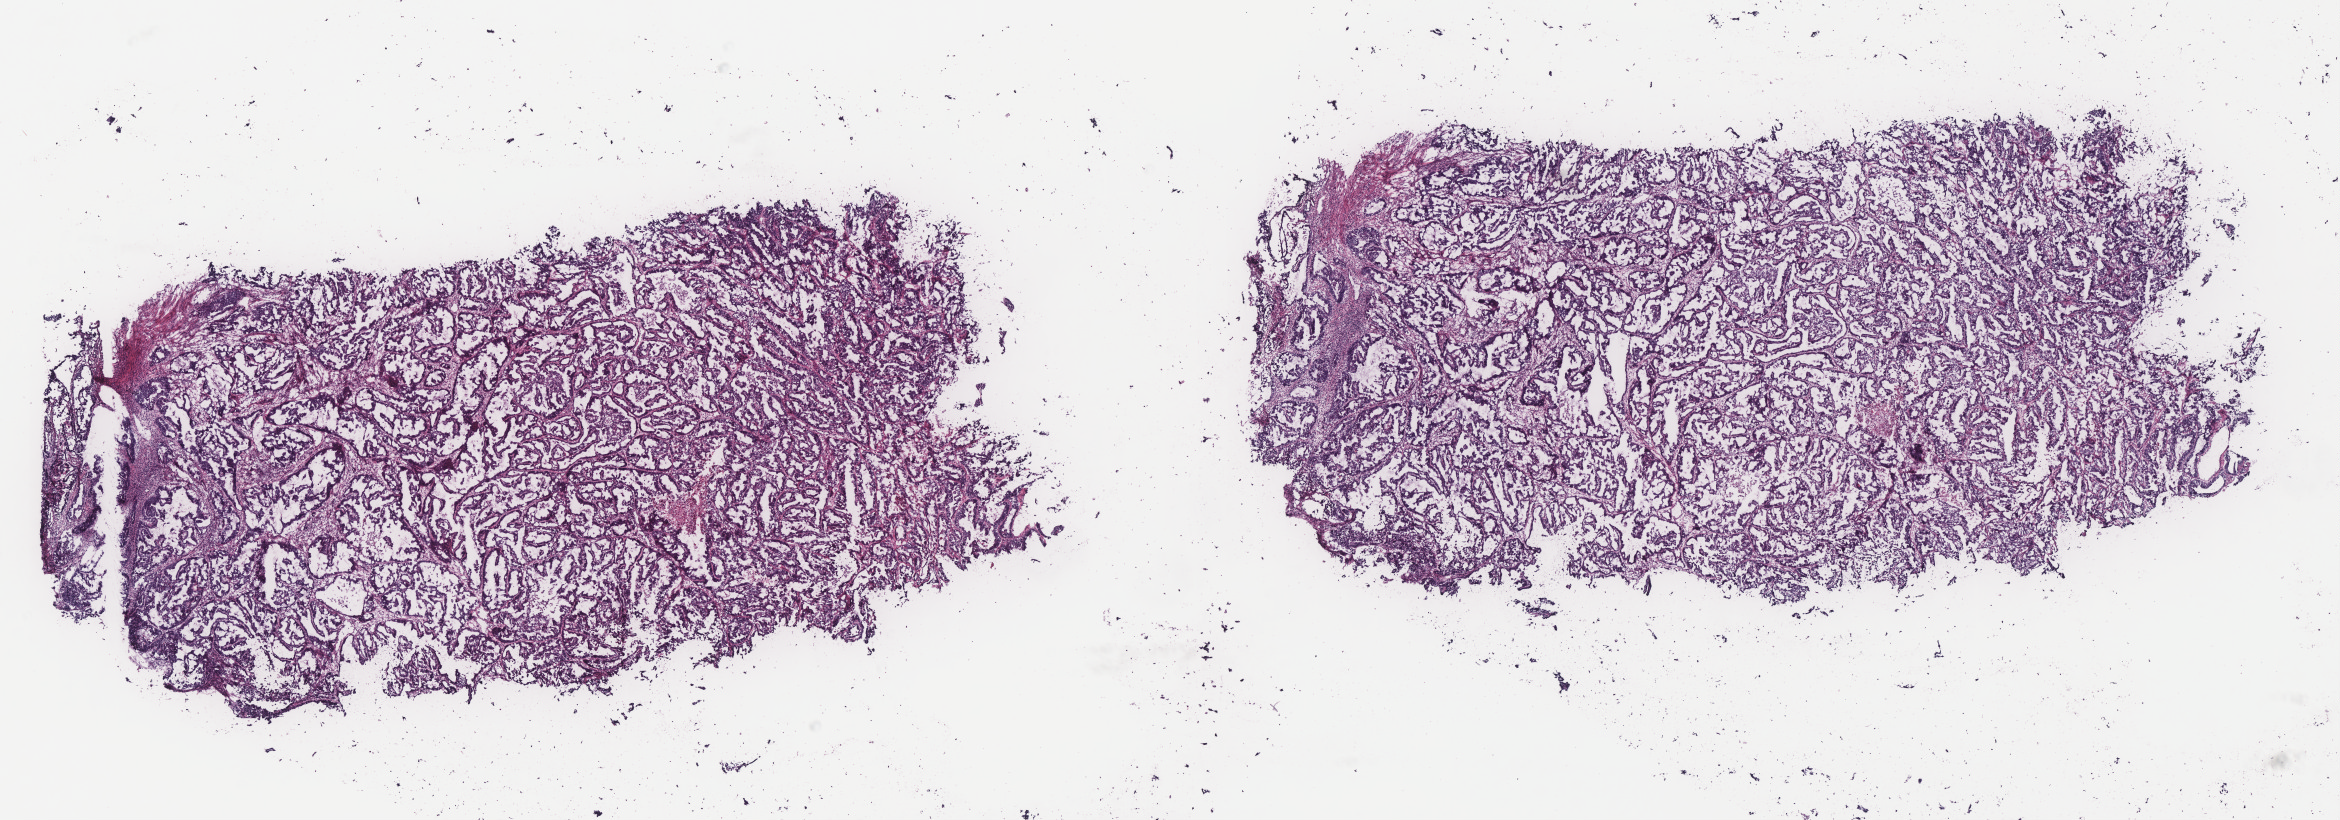
Whole-slide histology image, H&E, shown as a low-resolution overview of the whole scanned area (about 18.8 x 6.6 mm). Frozen section from the top of the tissue portion. Uterus, primary tumour sample. Female patient; age at initial diagnosis 67 years. Histologic grade: G3 (poorly differentiated). Slide review estimates, as recorded: tumour cells 60%, tumour nuclei 80%, normal cells 0%, stromal cells 20%, necrosis 20%. Infiltration values recorded for this section: lymphocyte infiltration 10%, monocyte infiltration 10%, neutrophil infiltration 10%.
FIGO stage: IIIA. Diagnosis: Serous cystadenocarcinoma, NOS (endometrium).